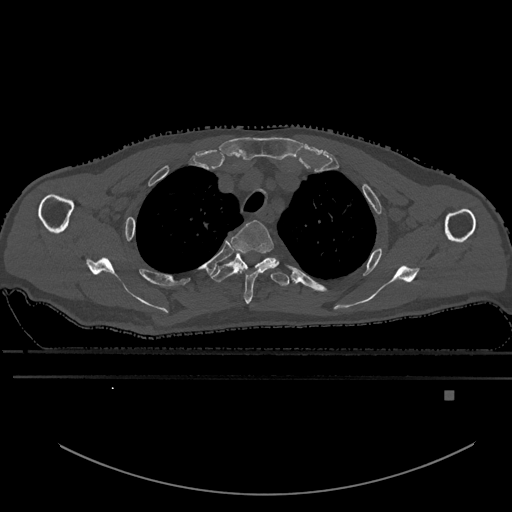
CT including the spine, one axial slice. Bone window (W 1800 / L 400 HU). 512 × 512 image matrix, field of view 456 × 456 mm. Patient: male, 82 years. Case-level facts recorded for this patient, not image findings: primary cancer: prostate; vertebrae with lytic lesions (as recorded): T11, T9, T8, T2.
Outlined on this slice (semi-automatic segmentation, software-assisted and operator-edited):
- T2 vertebra: bounding box <230,220,280,304> (left, top, right, bottom; pixels)
- T3 vertebra: <211,251,289,287>